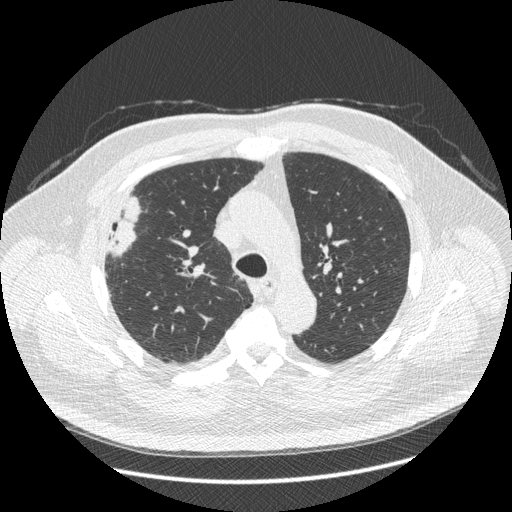
Chest CT (low-dose screening protocol), one axial image; third screening round (two years after baseline); lung window (W 1500 / L -600 HU); 1.25 mm slice thickness; standard (soft-tissue) reconstruction kernel (STANDARD); 120 kVp; slice 126 of 426 in the series. Male, age 66 years at enrolment.
• Expert reader's lesion annotation, bounding box [x1, y1, x2, y2] px = [87, 201, 147, 269].
• Reader record for this screening exam (exam-level; its link to the box is not recorded): non-calcified nodule or mass ≥4 mm, right upper lobe, 48 × 25 mm, spiculated (stellate) margins, soft tissue attenuation, pre-existing on the prior screen: no.
• Participant outcome: lung cancer diagnosed 35 days after this screen — non-small cell carcinoma, right upper lobe, stage IV (AJCC 6th edition), 50 mm at pathology.